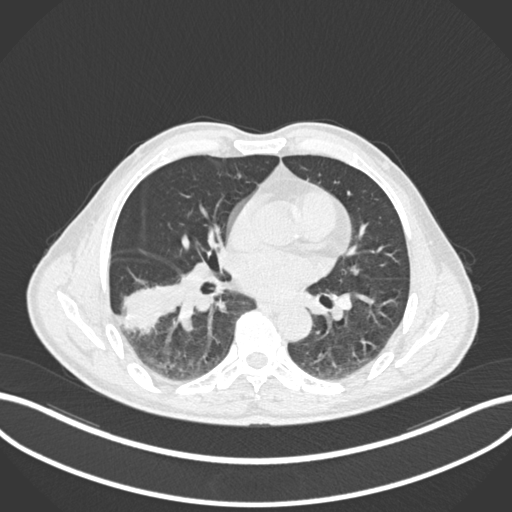
Chest CT, one axial slice. Slice 93 of 208 in the series (ordered by position). 120 kVp. Lung window (W 1500 / L -600 HU). 512 × 512 image matrix, field of view 400 × 400 mm. Patient: male, 58 years. From the clinical record (not read from this slice): clinical TNM (as recorded): T3 N0 M0; histopathological grade: G2.
Annotated regions visible in this slice (rectangle marked by the reading radiologist):
- lung tumour (recorded histology: squamous cell carcinoma): box from (x=120, y=276) to (x=180, y=336) px